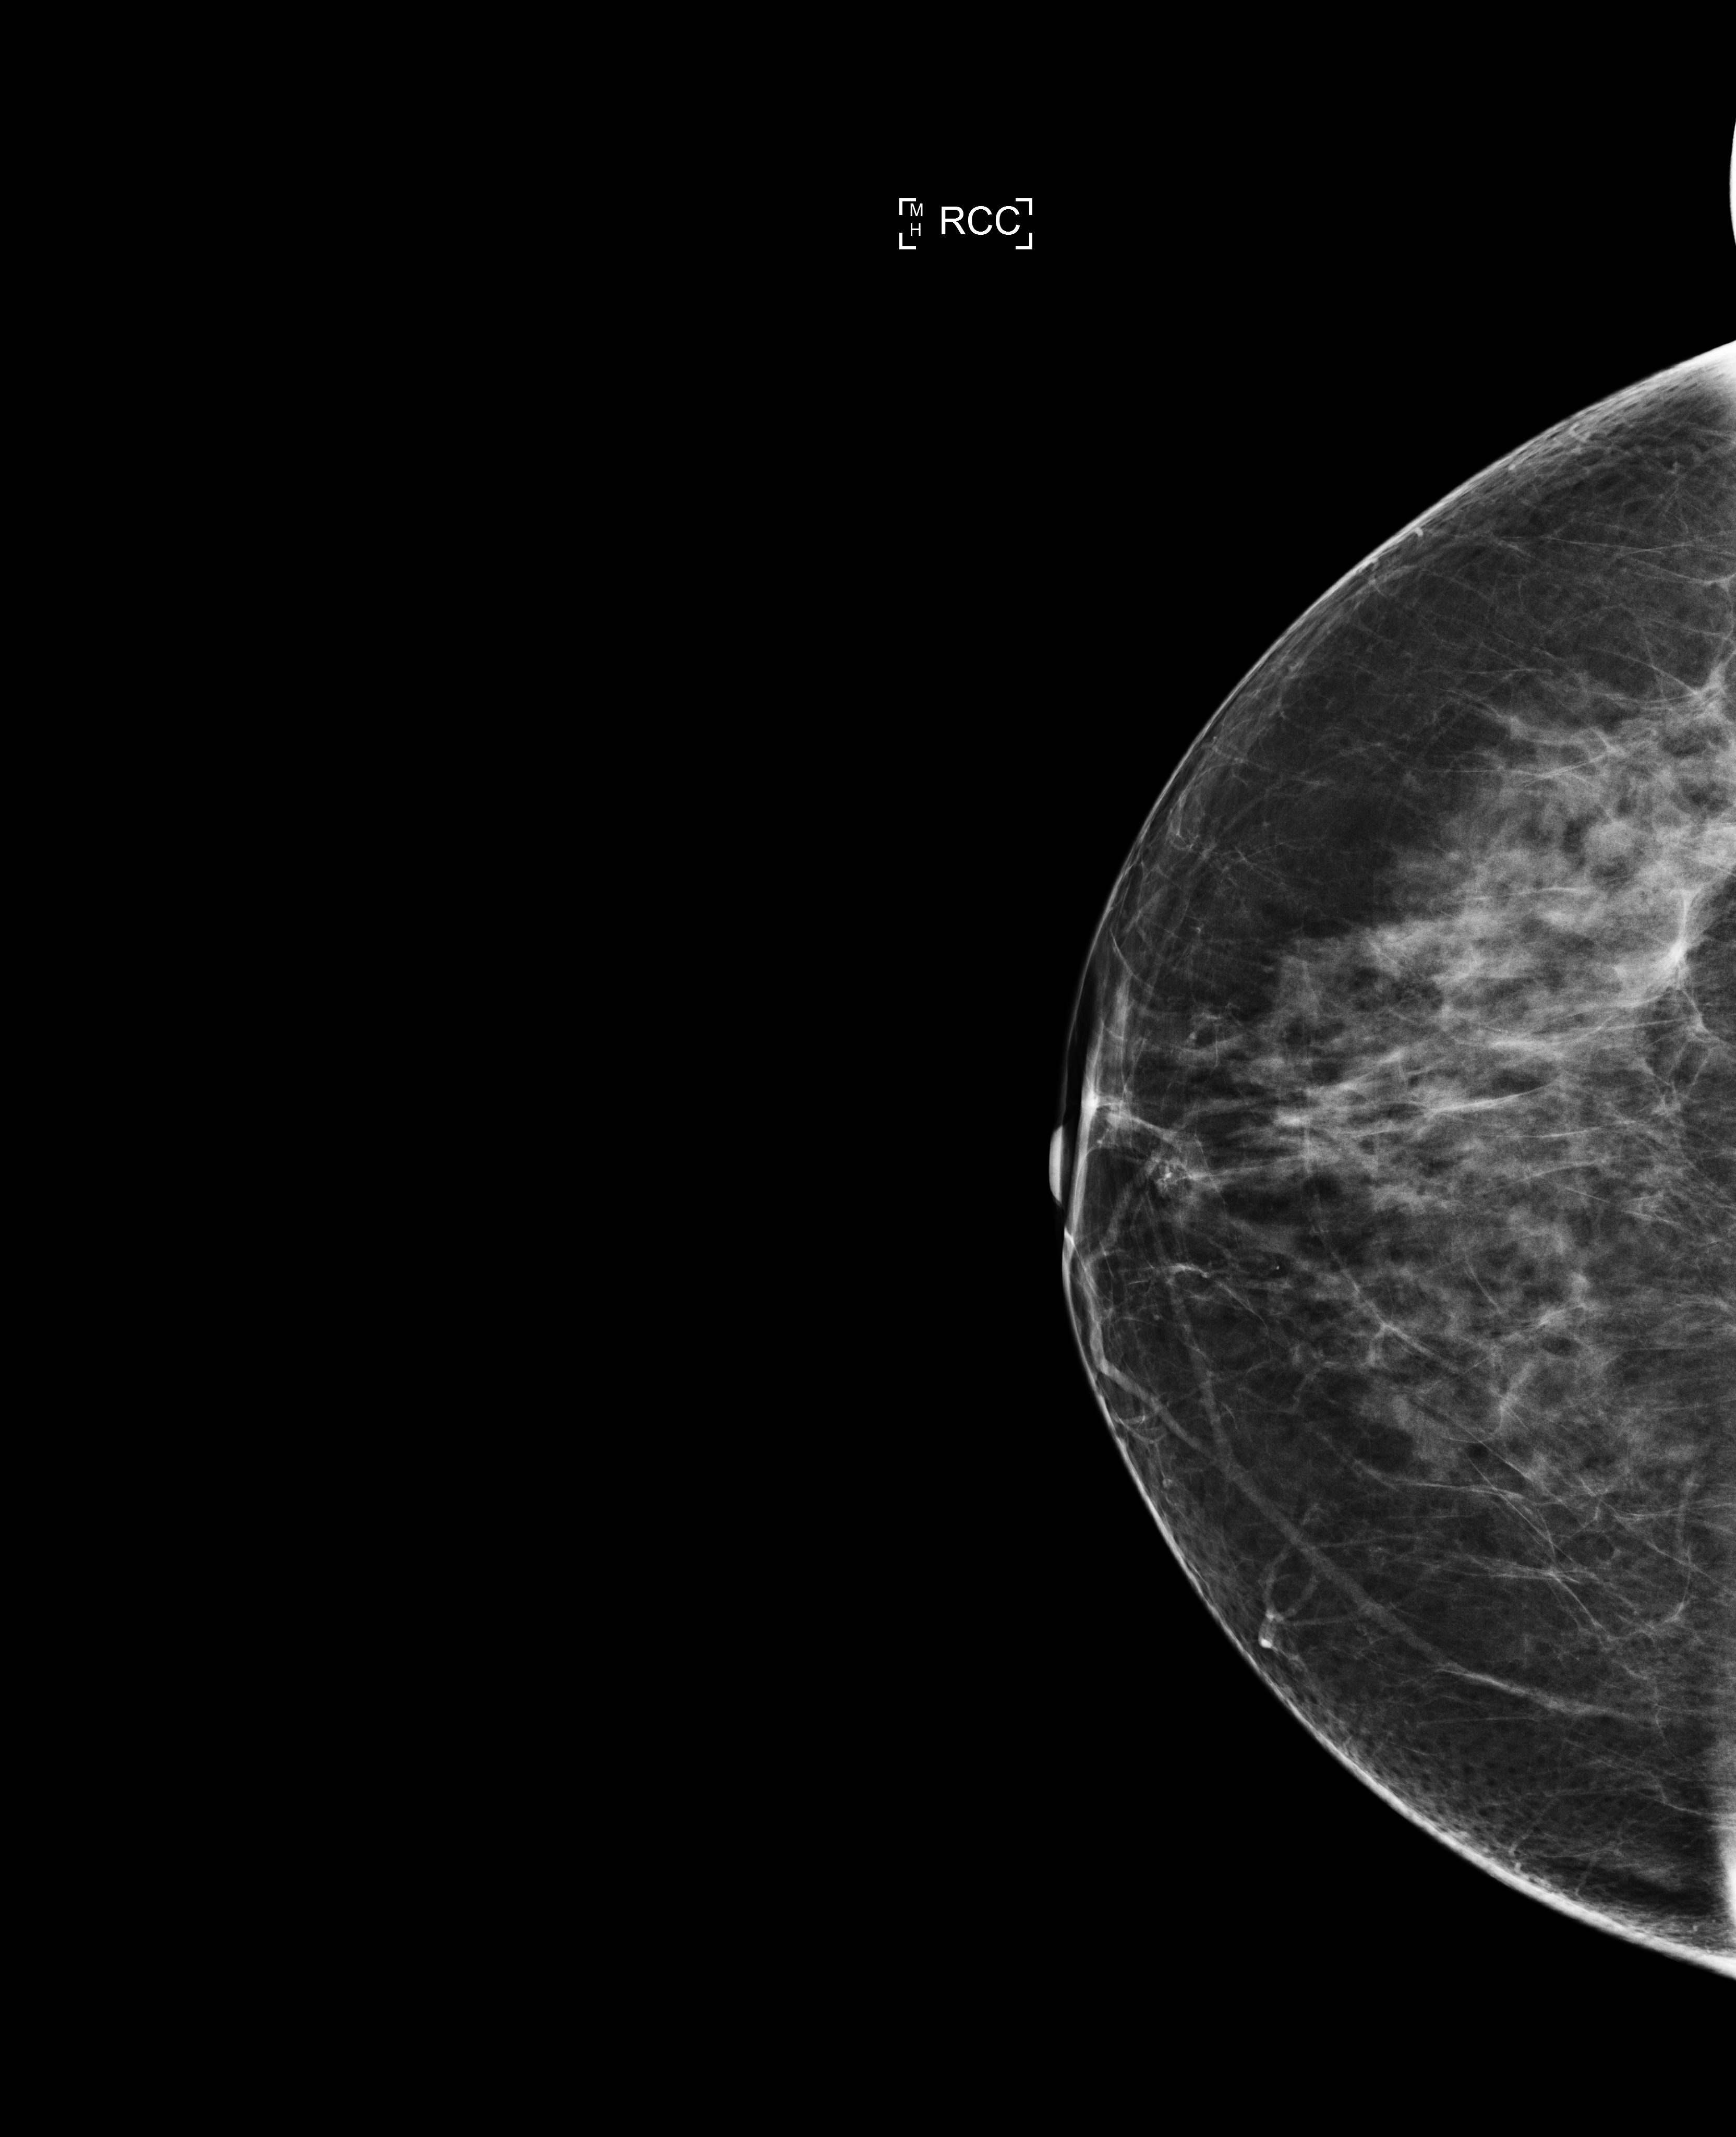
Screening examination; compressed breast thickness 63 mm; system: Selenia Dimensions. Female patient, age 57 years.
Image type: full-field digital mammogram. Breast: right. Projection: cranio-caudal projection.